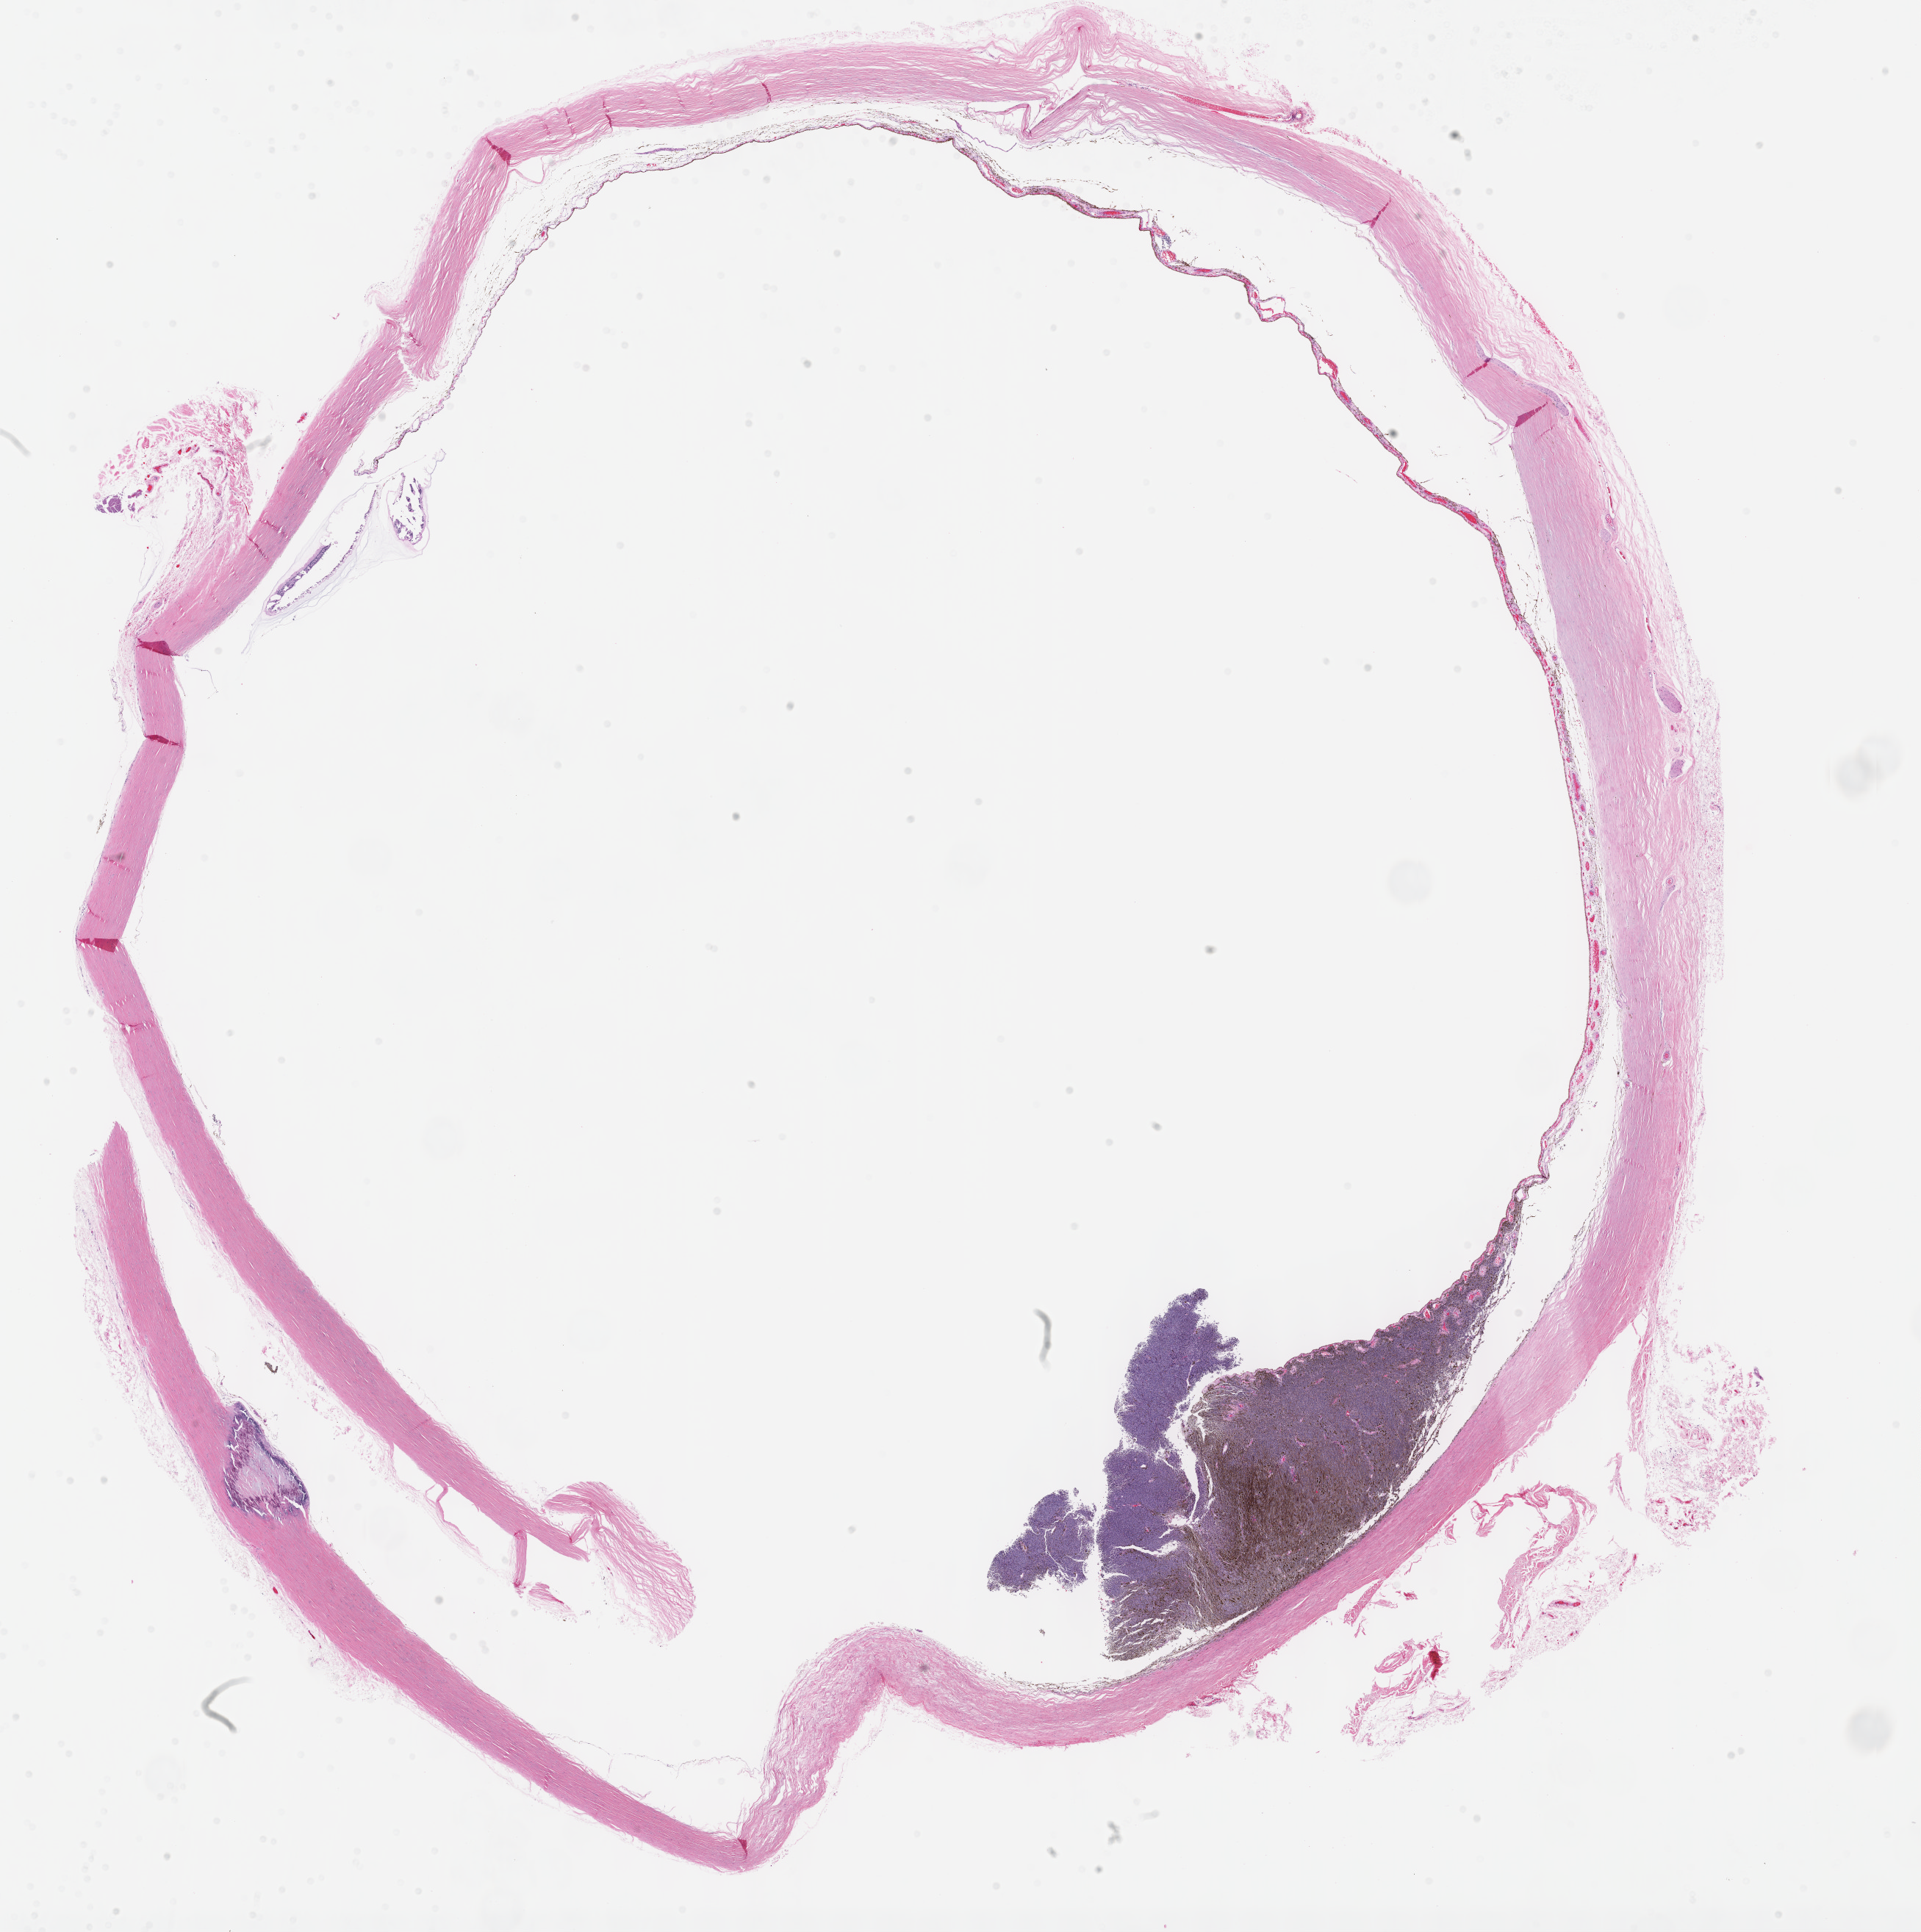
Whole-slide histology image, Hematoxylin and eosin (H&E) stained — shown as a low-resolution overview of the whole scanned area (about 21.1 x 21.3 mm). Formalin-fixed paraffin-embedded (FFPE) diagnostic section. Uvea, primary tumour sample. Male, age 60 years at initial diagnosis.
Pathologic diagnosis: Spindle cell melanoma, NOS (choroid). AJCC pathologic stage: IIA (7th edition).